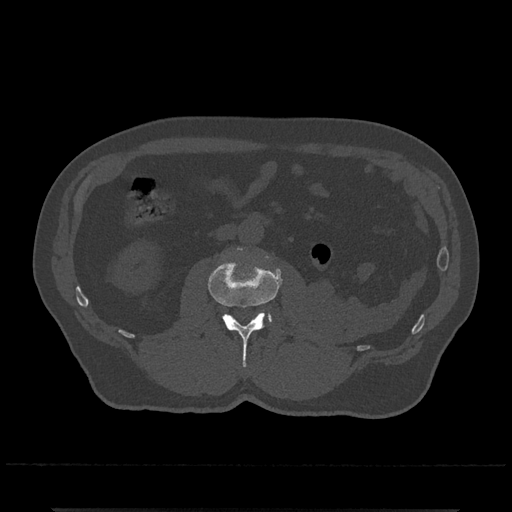
CT including the spine, one axial slice; position 280 of 797 along the scan axis; reconstruction kernel Br40s/3; bone window (W 1800 / L 400 HU); 0.5 mm slice thickness; 512 × 512 image matrix, field of view 393 × 393 mm. Male patient, age 67 years. From the clinical record (not read from this slice): primary cancer: prostate.
Annotated regions visible in this slice (semi-automatically segmented with operator editing):
- L2 vertebra: bounding box (x1, y1, x2, y2) in pixels: (208, 247, 282, 367)
- L3 vertebra: (258, 312, 272, 323)